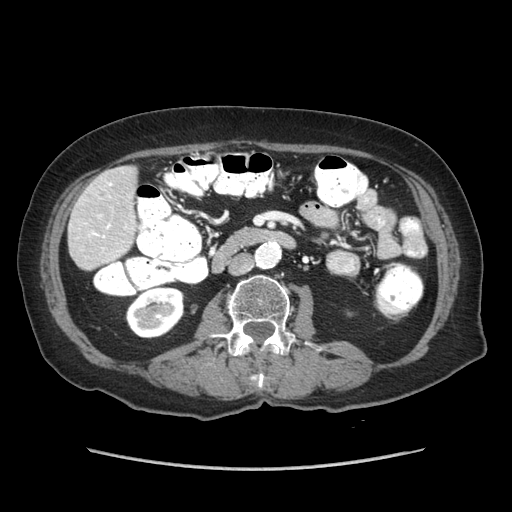
Contrast-enhanced abdominal CT (liver protocol), one axial slice. Position 15 of 89 along the scan axis. Soft-tissue window (W 400 / L 40 HU). 512 × 512 image matrix. Case-level facts recorded for this patient, not image findings: diagnosis: hepatocellular carcinoma (patient treated with transarterial chemoembolisation; whether this scan precedes or follows treatment is not stated here); TNM stage (as recorded): Stage-IIIA; Child-Pugh class: A; tumour nodularity: multinodular; tumour size: 11 cm.
Structures marked on this image (semi-automatically segmented with operator editing):
- liver parenchyma outside the tumour (the mass and vessels are separate outlines, so this box may not span the whole liver): bounding box [x1, y1, x2, y2] px = [68, 166, 136, 270]
- liver vessels: [91, 183, 112, 237]